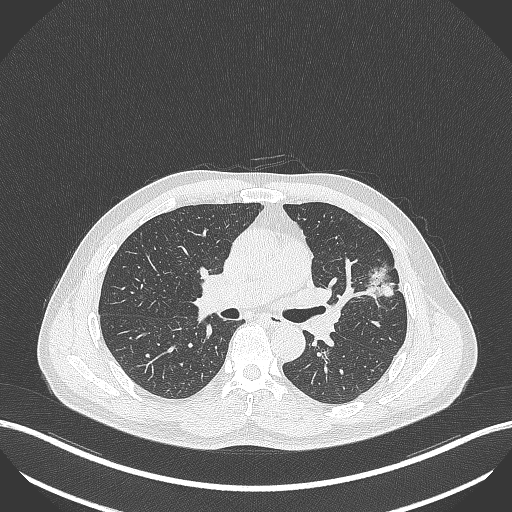
Chest CT, one axial slice. Position 229 of 418 along the scan axis. 120 kVp. Lung window (W 1500 / L -600 HU). 1 mm slice thickness. 512 × 512 image matrix, field of view 400 × 400 mm. Male patient, age 55 years. From the clinical record (not read from this slice): clinical TNM (as recorded): T1c N0 M0; histopathological grade: G2-3.
Outlined on this slice (rectangle marked by the reading radiologist):
- lung tumour (recorded histology: adenocarcinoma): bounding box <362,262,398,299> (left, top, right, bottom; pixels)